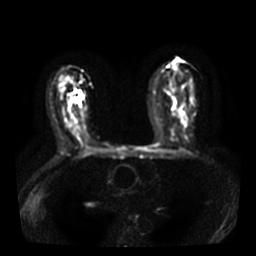
Breast MRI, one axial slice. Slice 18 of 36 in the series (ordered by position). Diffusion-weighted series; image 2 of 4 stored at this slice position (different b-values; order by instance number). 3 T. 256 × 256 image matrix, field of view 320 × 320 mm. Female patient.
Annotated regions visible in this slice (manually delineated by an expert):
- tumour on diffusion-weighted imaging: bounding box [x1, y1, x2, y2] px = [78, 93, 81, 99]